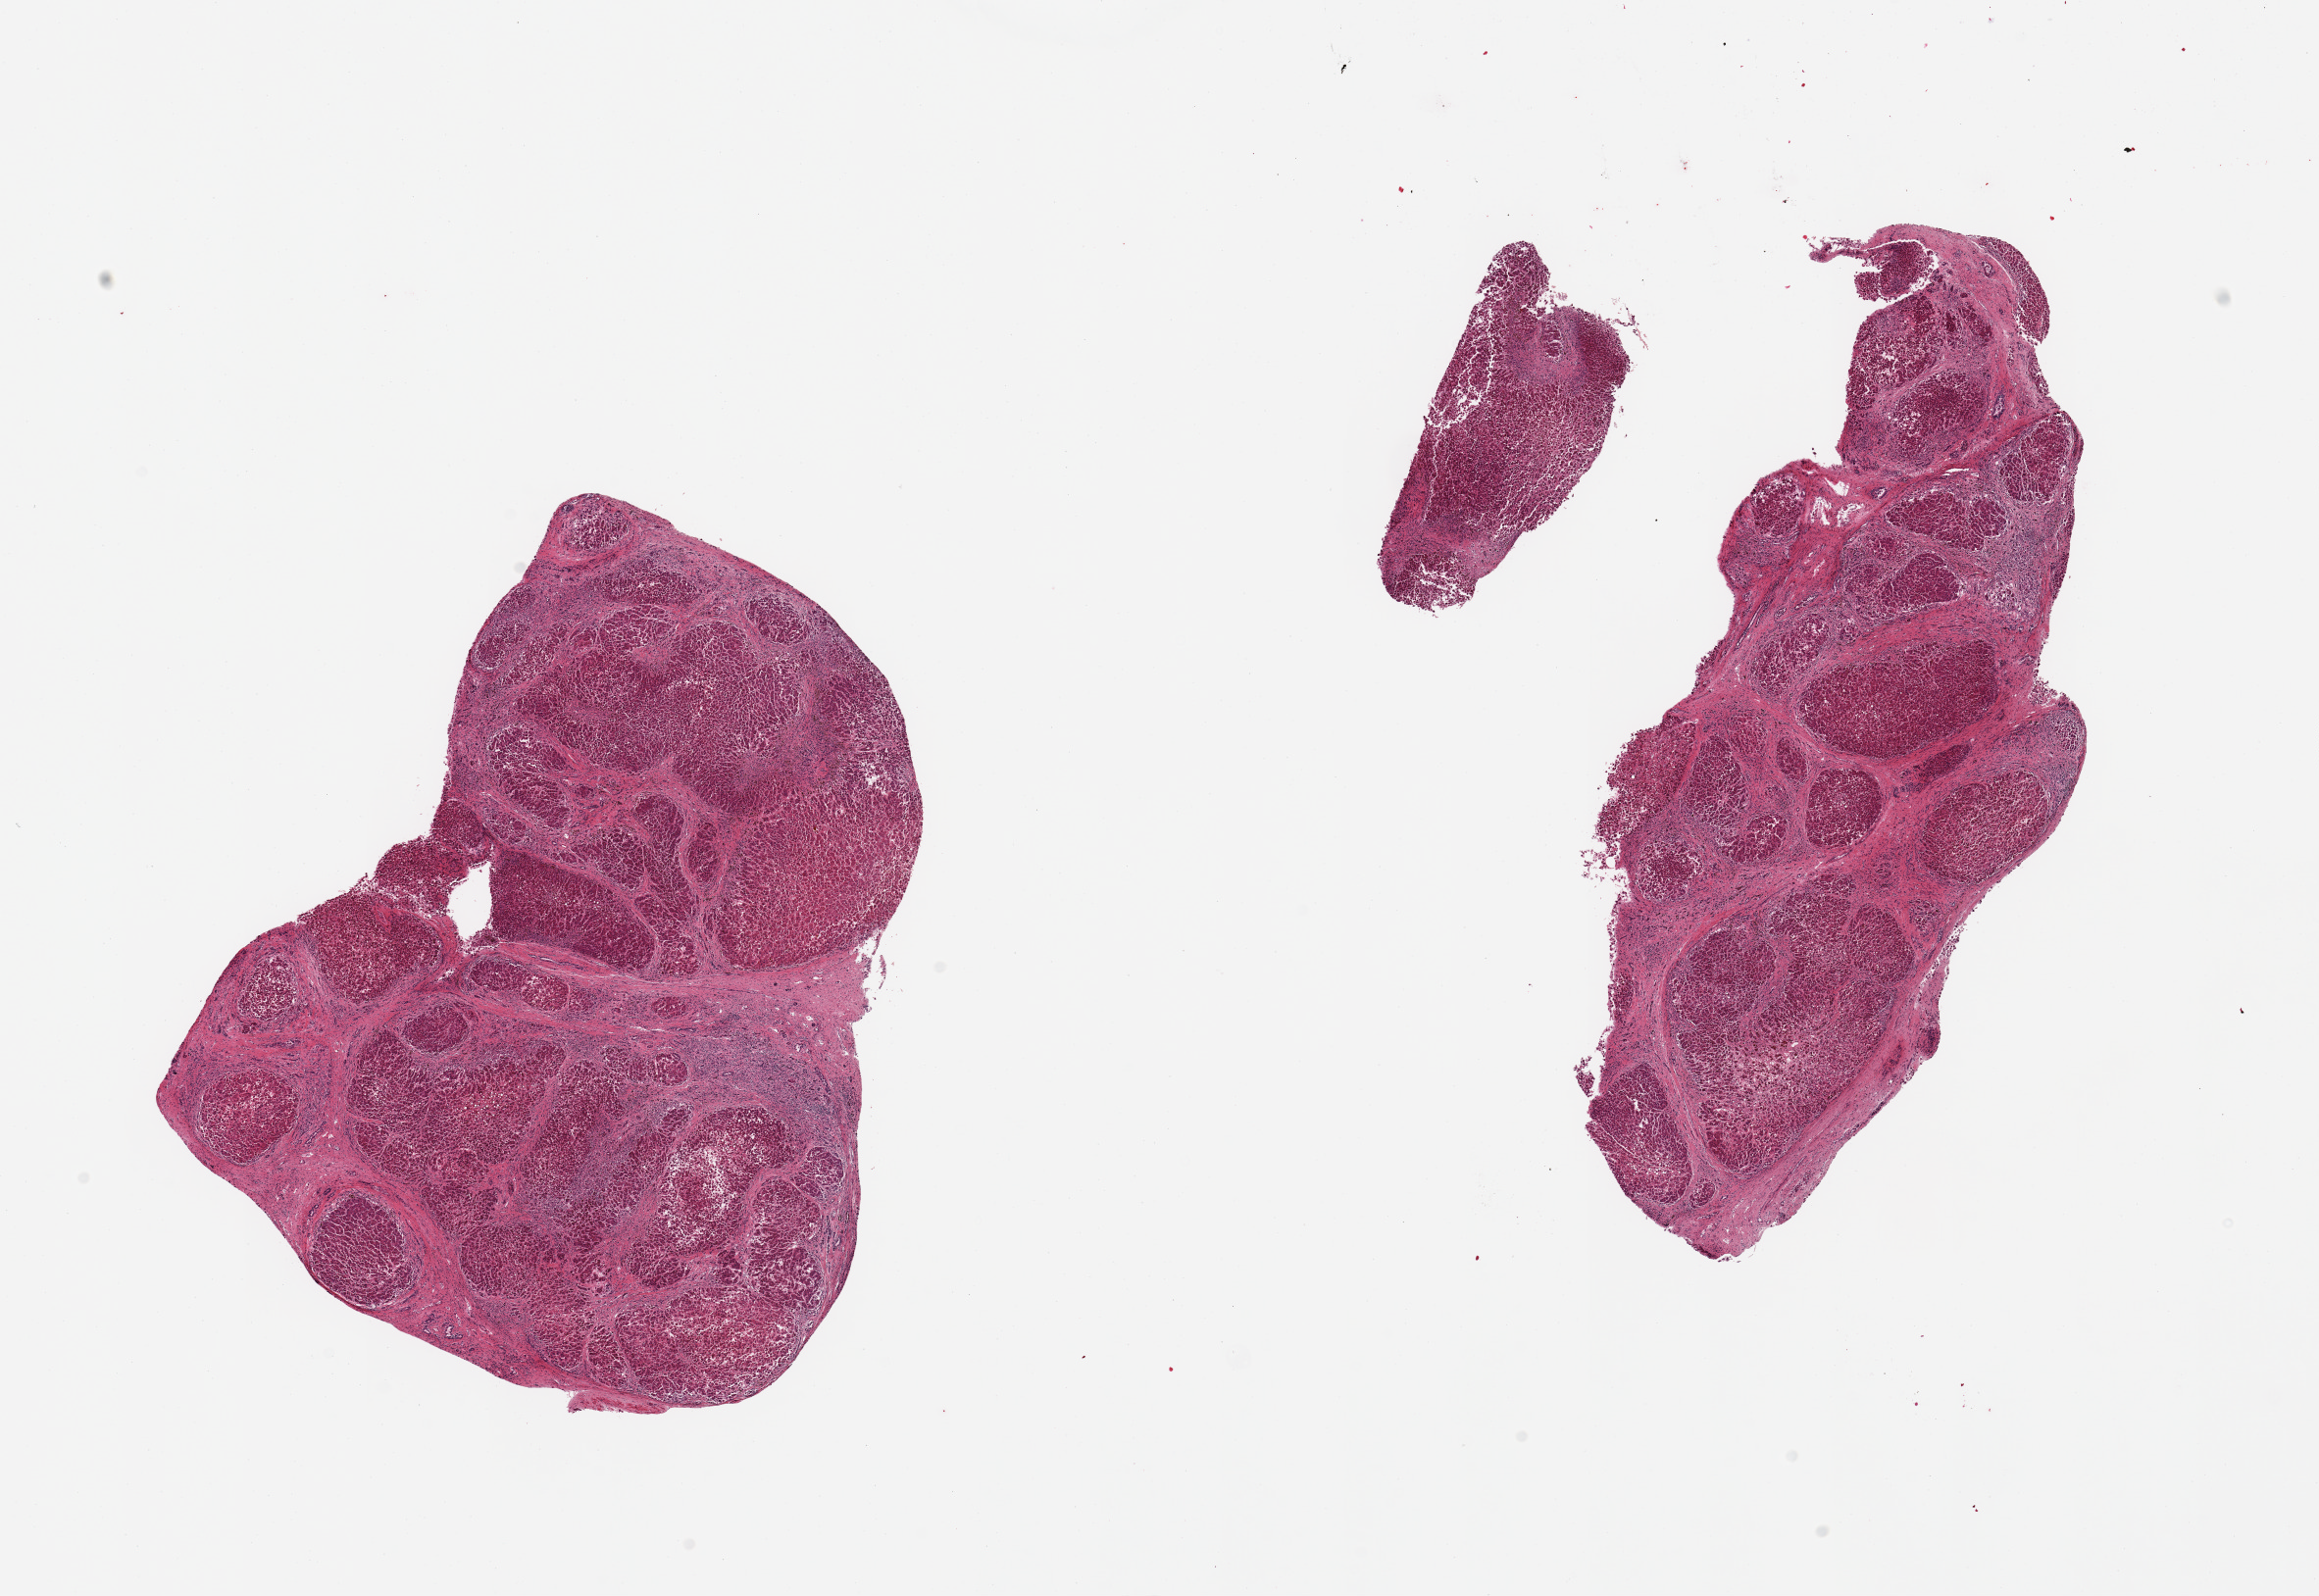
Whole-slide image, haematoxylin and eosin stain — a low-resolution overview of the entire scanned area, about 18.7 x 12.9 mm. PAXgene-fixed paraffin-embedded (PFPE) section. Target tissue: liver. Donor tissue sample. Male donor.
Reviewer comment on this tissue sample: 2 pieces, advanced cirrhosis/chronic hepatitis.